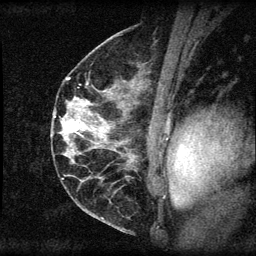
Breast MRI (dynamic contrast-enhanced), one sagittal slice. Slice 35 of 60 in the series (ordered by position). Dynamic contrast-enhanced series, image 2 of 3 at this slice position (ordered by acquisition). 1.5 T. TE 4.2 ms, TR 8.2 ms. 256 × 256 image matrix, field of view 180 × 180 mm. Patient: female, 45 years.
Annotated regions visible in this slice (semi-automatically segmented with operator editing):
- analysis volume of interest (the breast-tissue region the enhancement analysis was run in; not a lesion): bounding box [x1, y1, x2, y2] px = [55, 110, 94, 148]
- tumour enhancement mask (voxels above the 70 % enhancement threshold inside the analysis volume of interest): [72, 122, 84, 133]